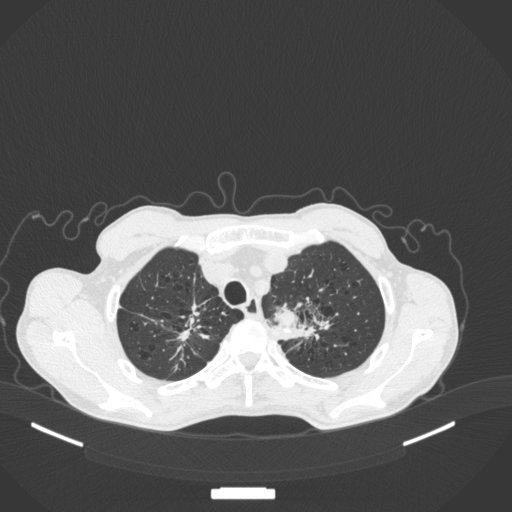
Chest CT, one axial slice; slice 362 of 394 in the series (ordered by position); reconstruction kernel B31f; 120 kVp; lung window (W 1500 / L -600 HU); 512 × 512 image matrix, field of view 400 × 400 mm. Male patient, age 65 years. Case-level facts recorded for this patient, not image findings: clinical TNM (as recorded): T2b N0 M0; histopathological grade: G2.
Structures marked on this image (bounding box drawn by a radiologist):
- lung tumour (recorded histology: adenocarcinoma): bounding box [x1, y1, x2, y2] px = [274, 301, 300, 330]